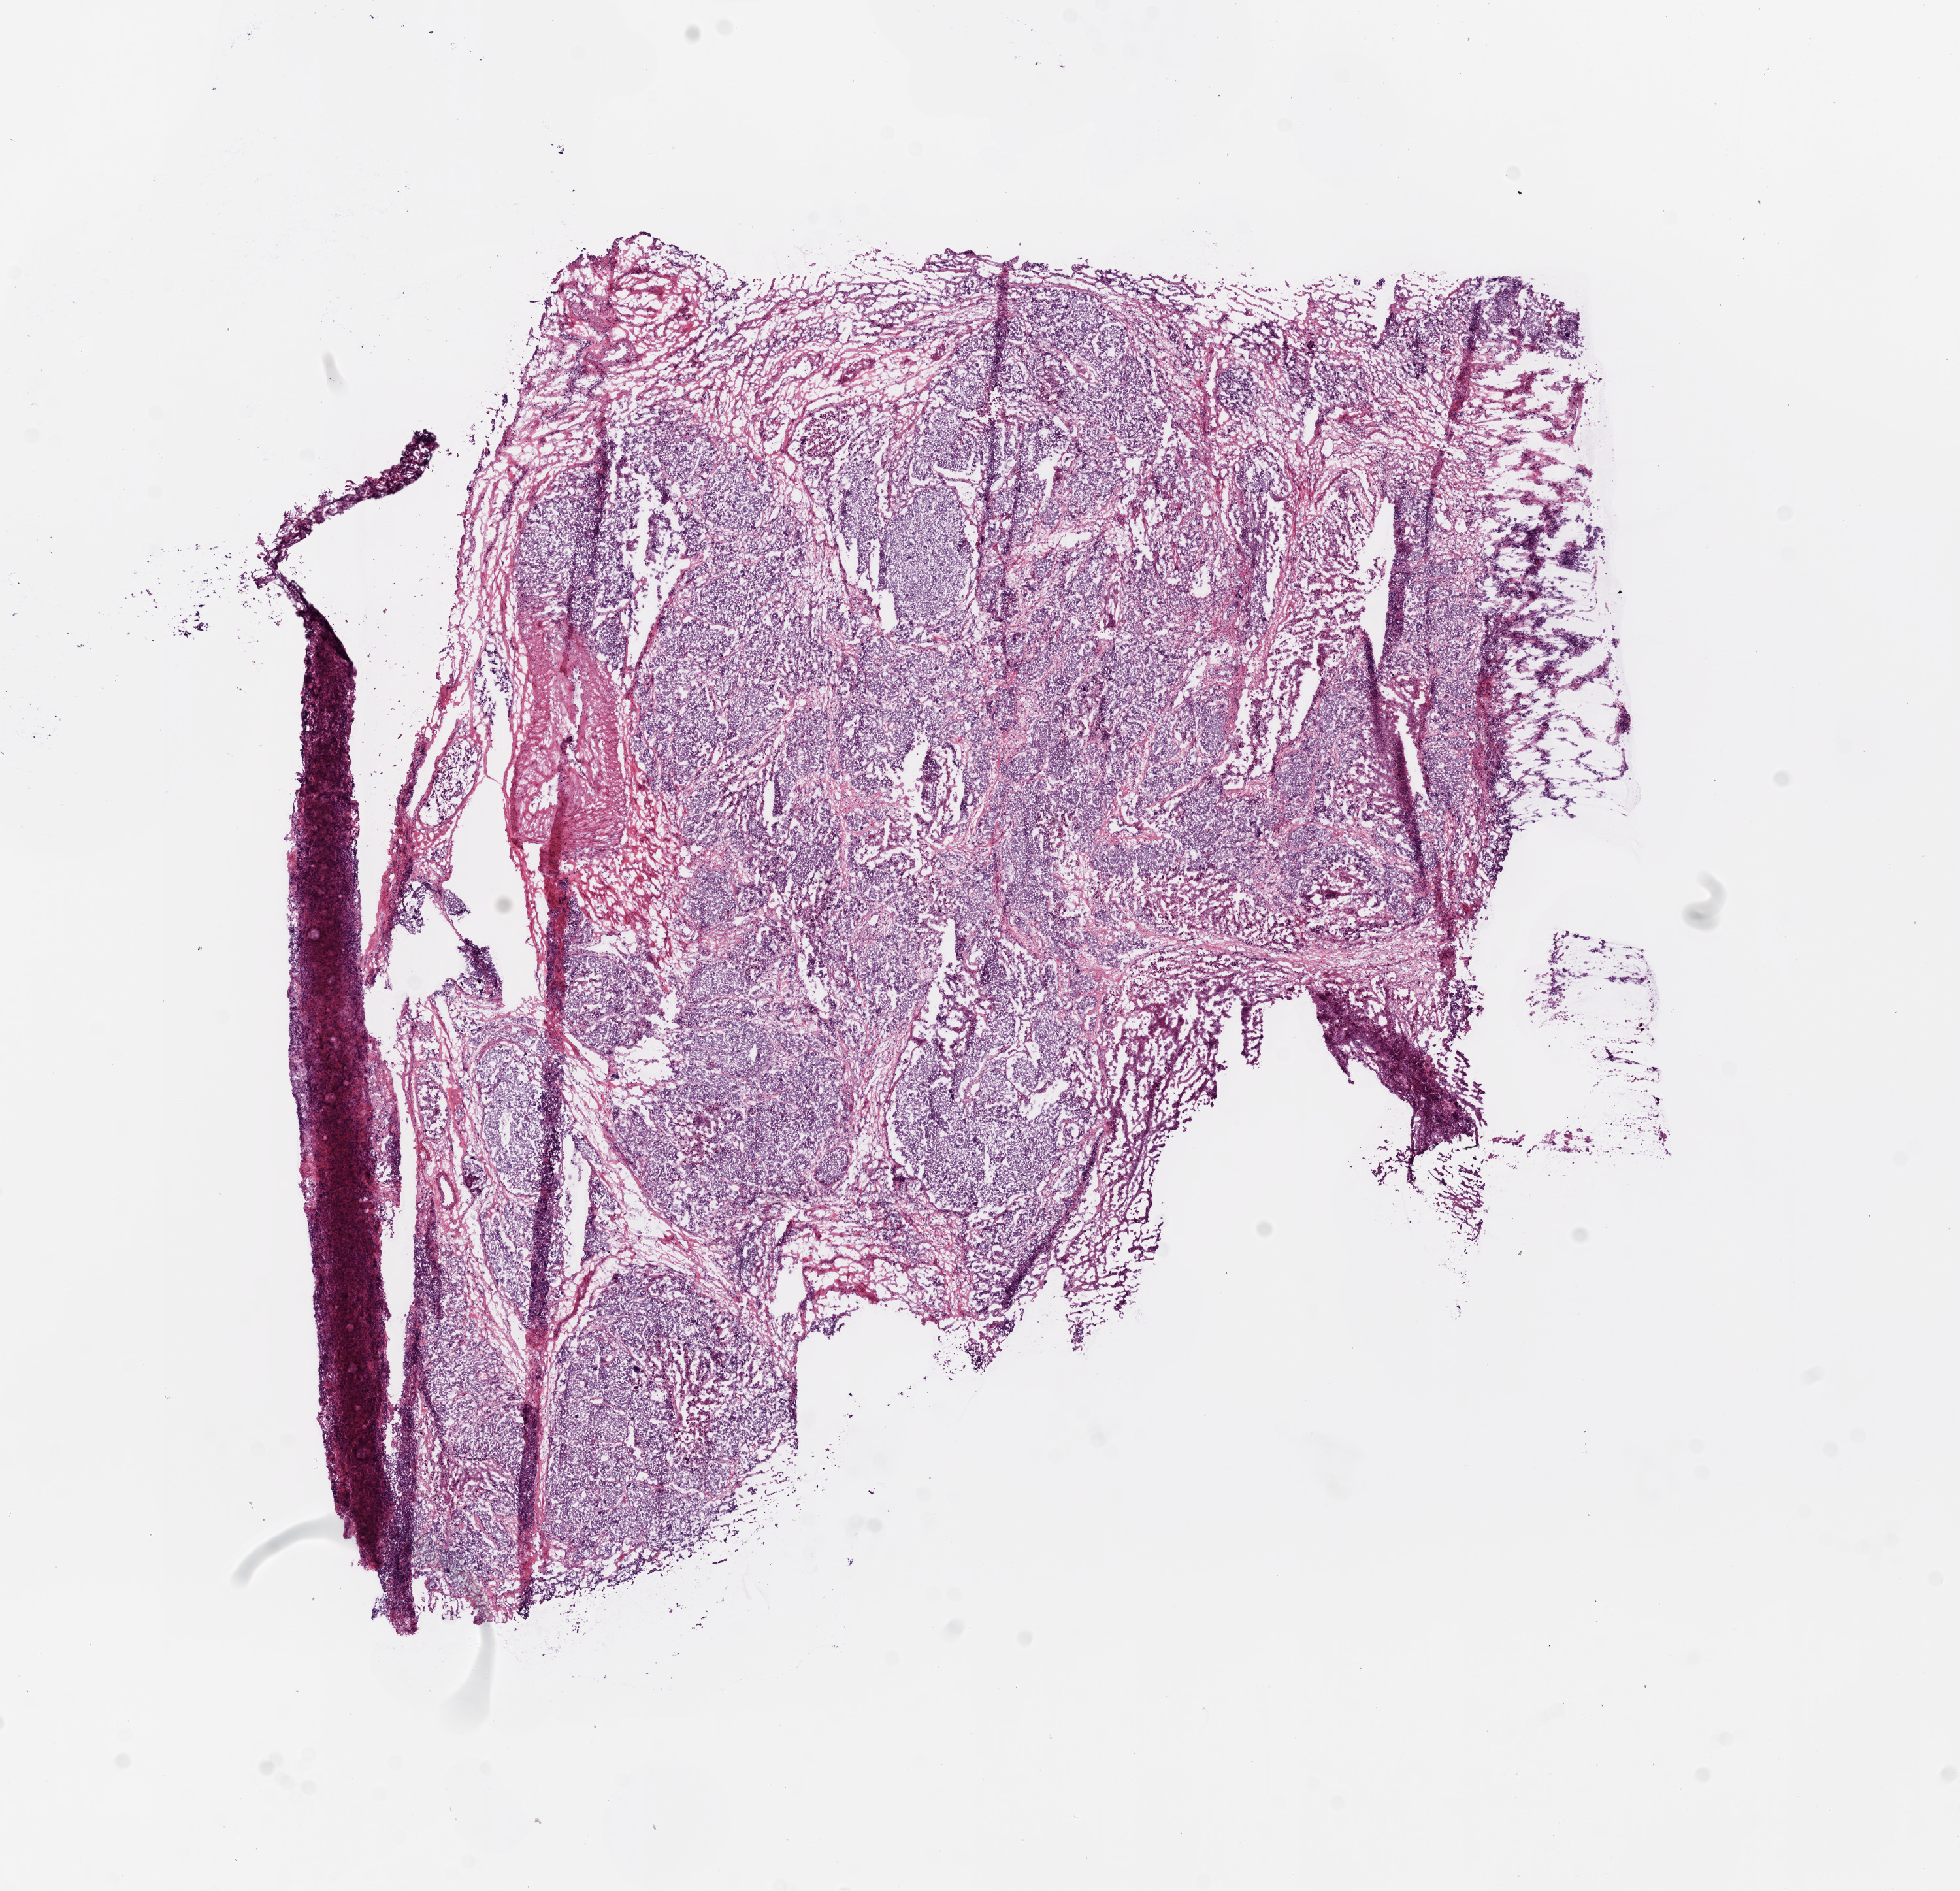
Digitized Hematoxylin and eosin (H&E) stained tissue section (whole slide), a low-resolution overview of the entire scanned area, about 12.0 x 11.6 mm; frozen section from the bottom of the tissue portion; ovary, primary tumour sample. Female, age 57 years at initial diagnosis. Histologic grade: G3 (poorly differentiated). Composition of this section per pathologist review: tumour cells 80%, tumour nuclei 90%, normal cells 1%, stromal cells 9%, necrosis 10%.
* FIGO stage: IIIC
* histologic diagnosis: Serous cystadenocarcinoma, NOS